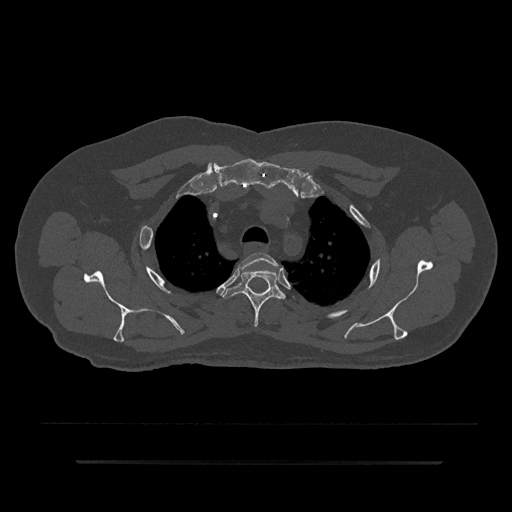
CT including the spine, one axial slice. Slice 664 of 797 in the series (ordered by position). Reconstruction kernel Br40s/3. 120 kVp. Bone window (W 1800 / L 400 HU). 512 × 512 image matrix. Male patient, age 59 years. From the clinical record (not read from this slice): primary cancer: bile ducts; vertebrae with lytic lesions (as recorded): T10.
Annotated regions visible in this slice (semi-automatically segmented with operator editing):
- T2 vertebra: bounding box <238,252,279,271> (left, top, right, bottom; pixels)
- T3 vertebra: <223,269,286,328>